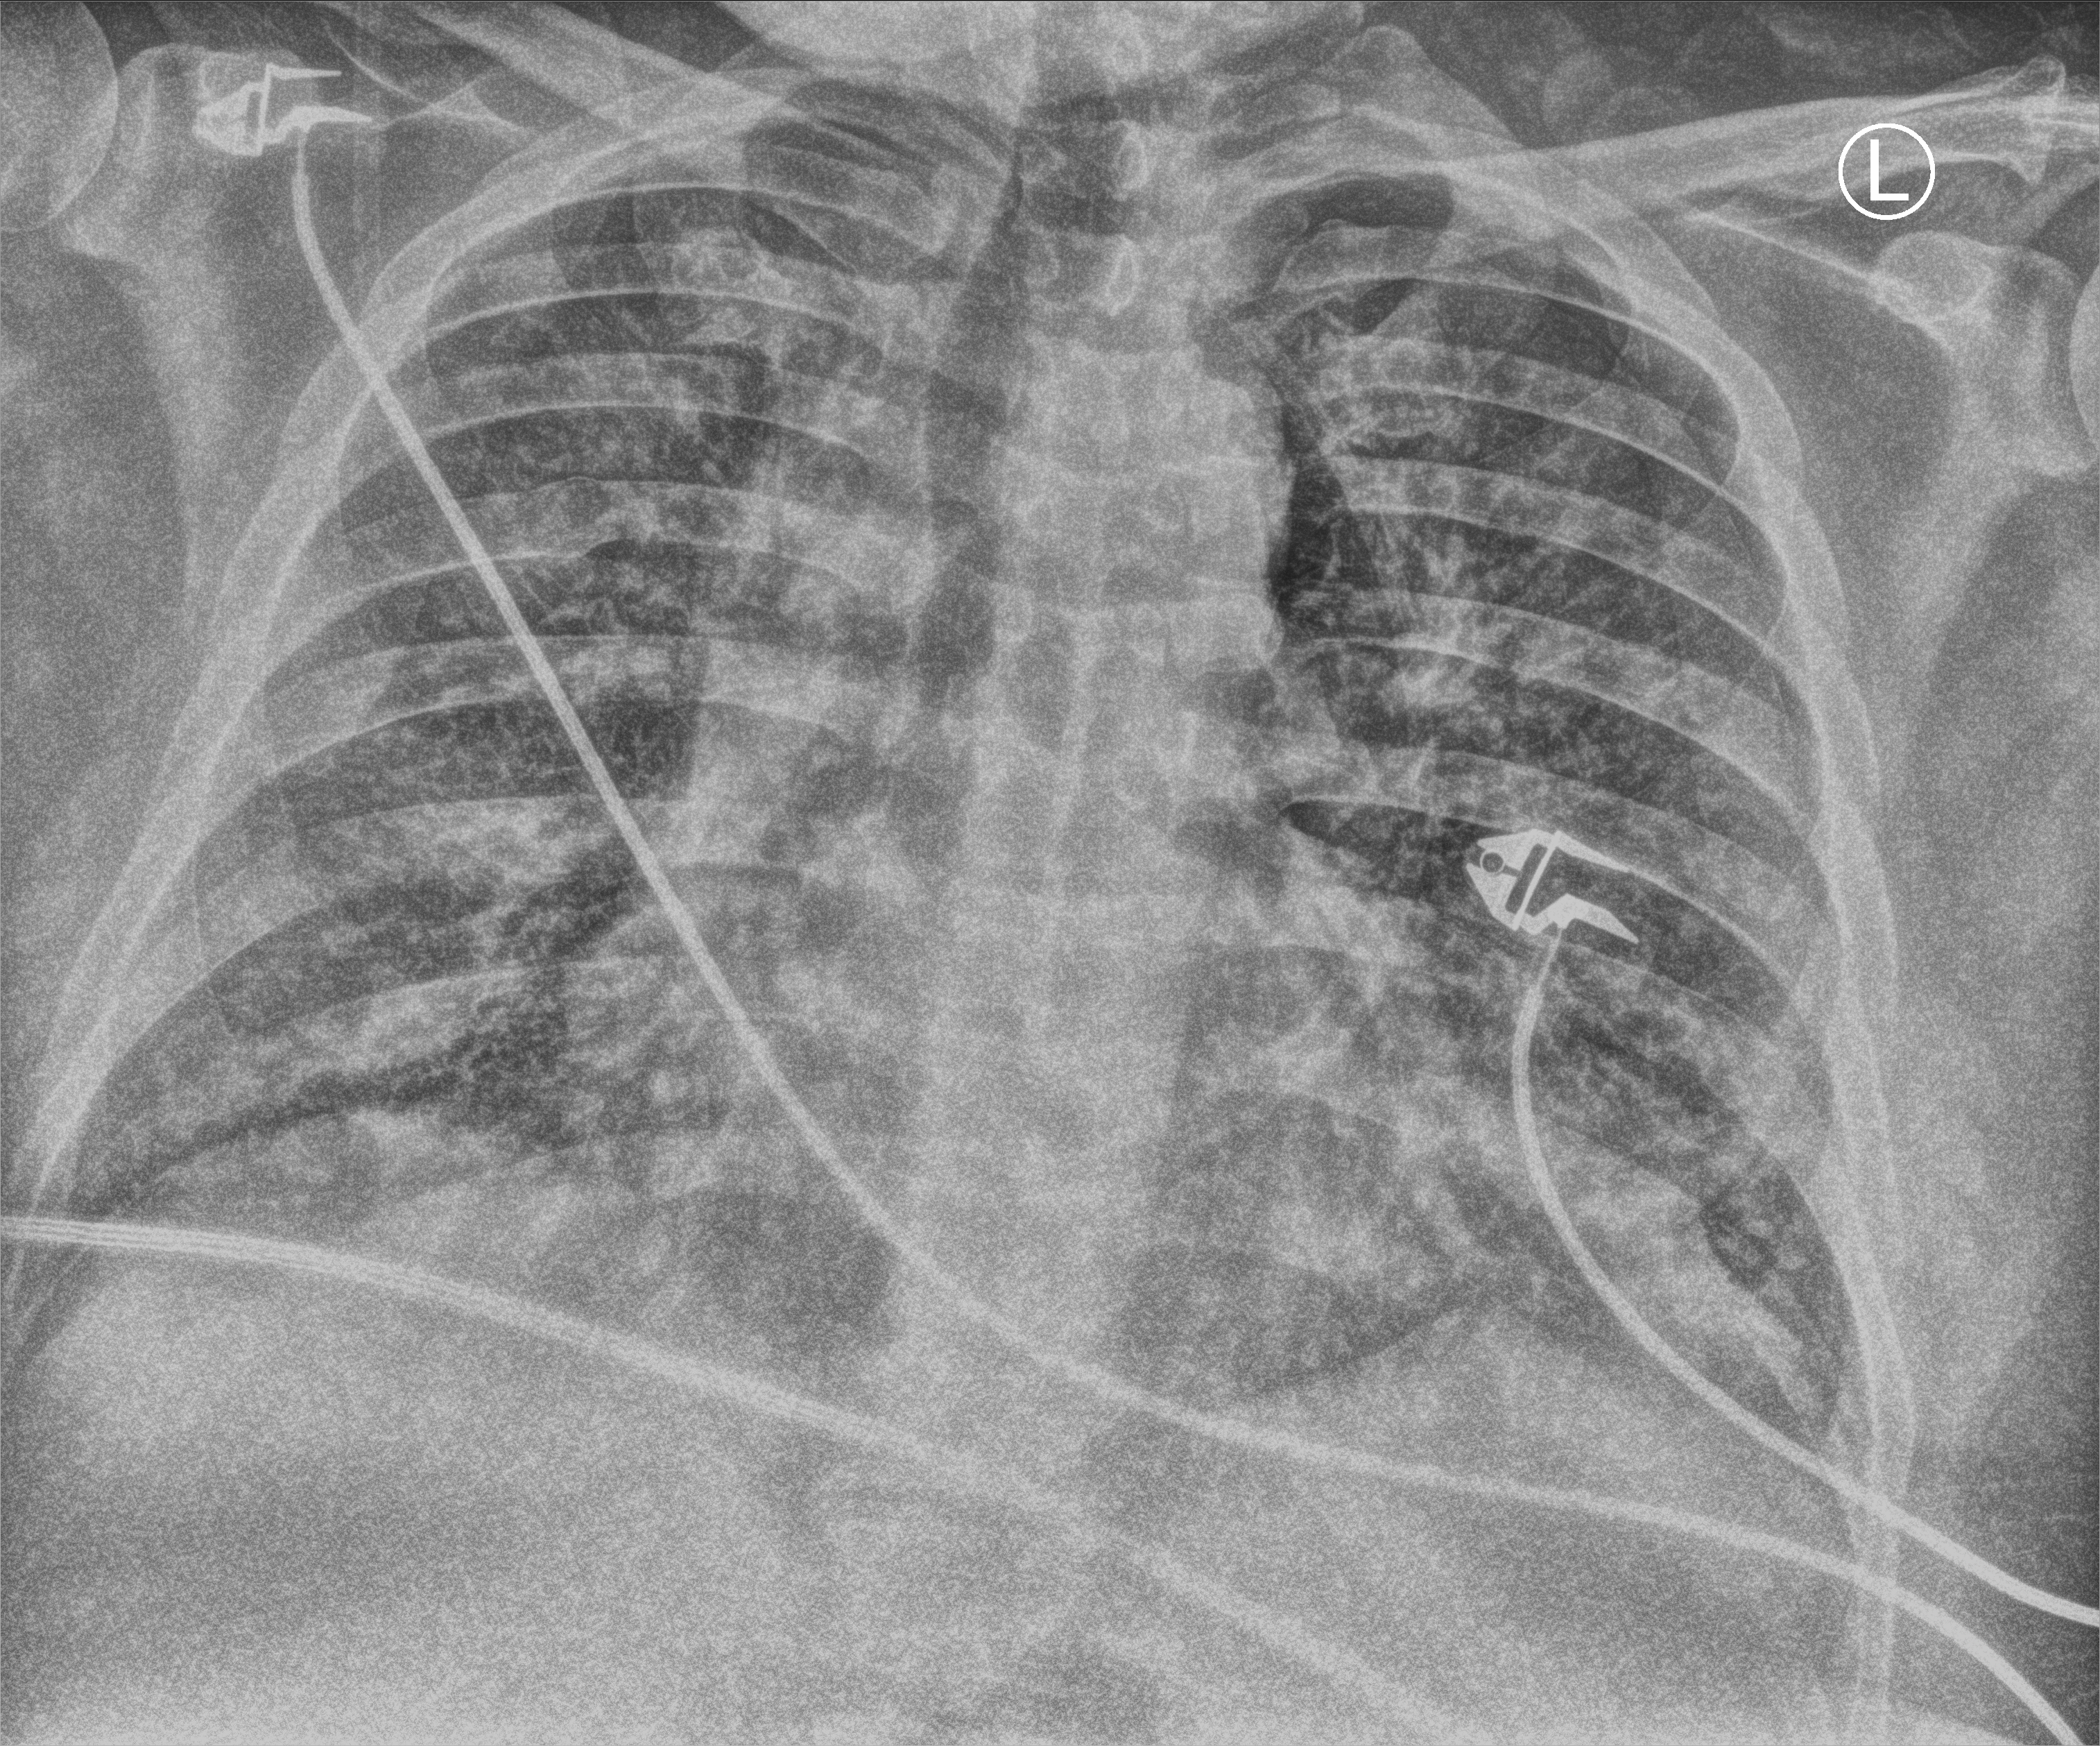
Portable chest radiograph. Patient hospitalised with COVID-19; male, aged 18–59 years.
From the hospital-stay record, not from the radiograph (when in the stay this image was taken is not recorded):
- admitted to intensive care during this hospital stay: yes
- chronic kidney disease (admission record): no